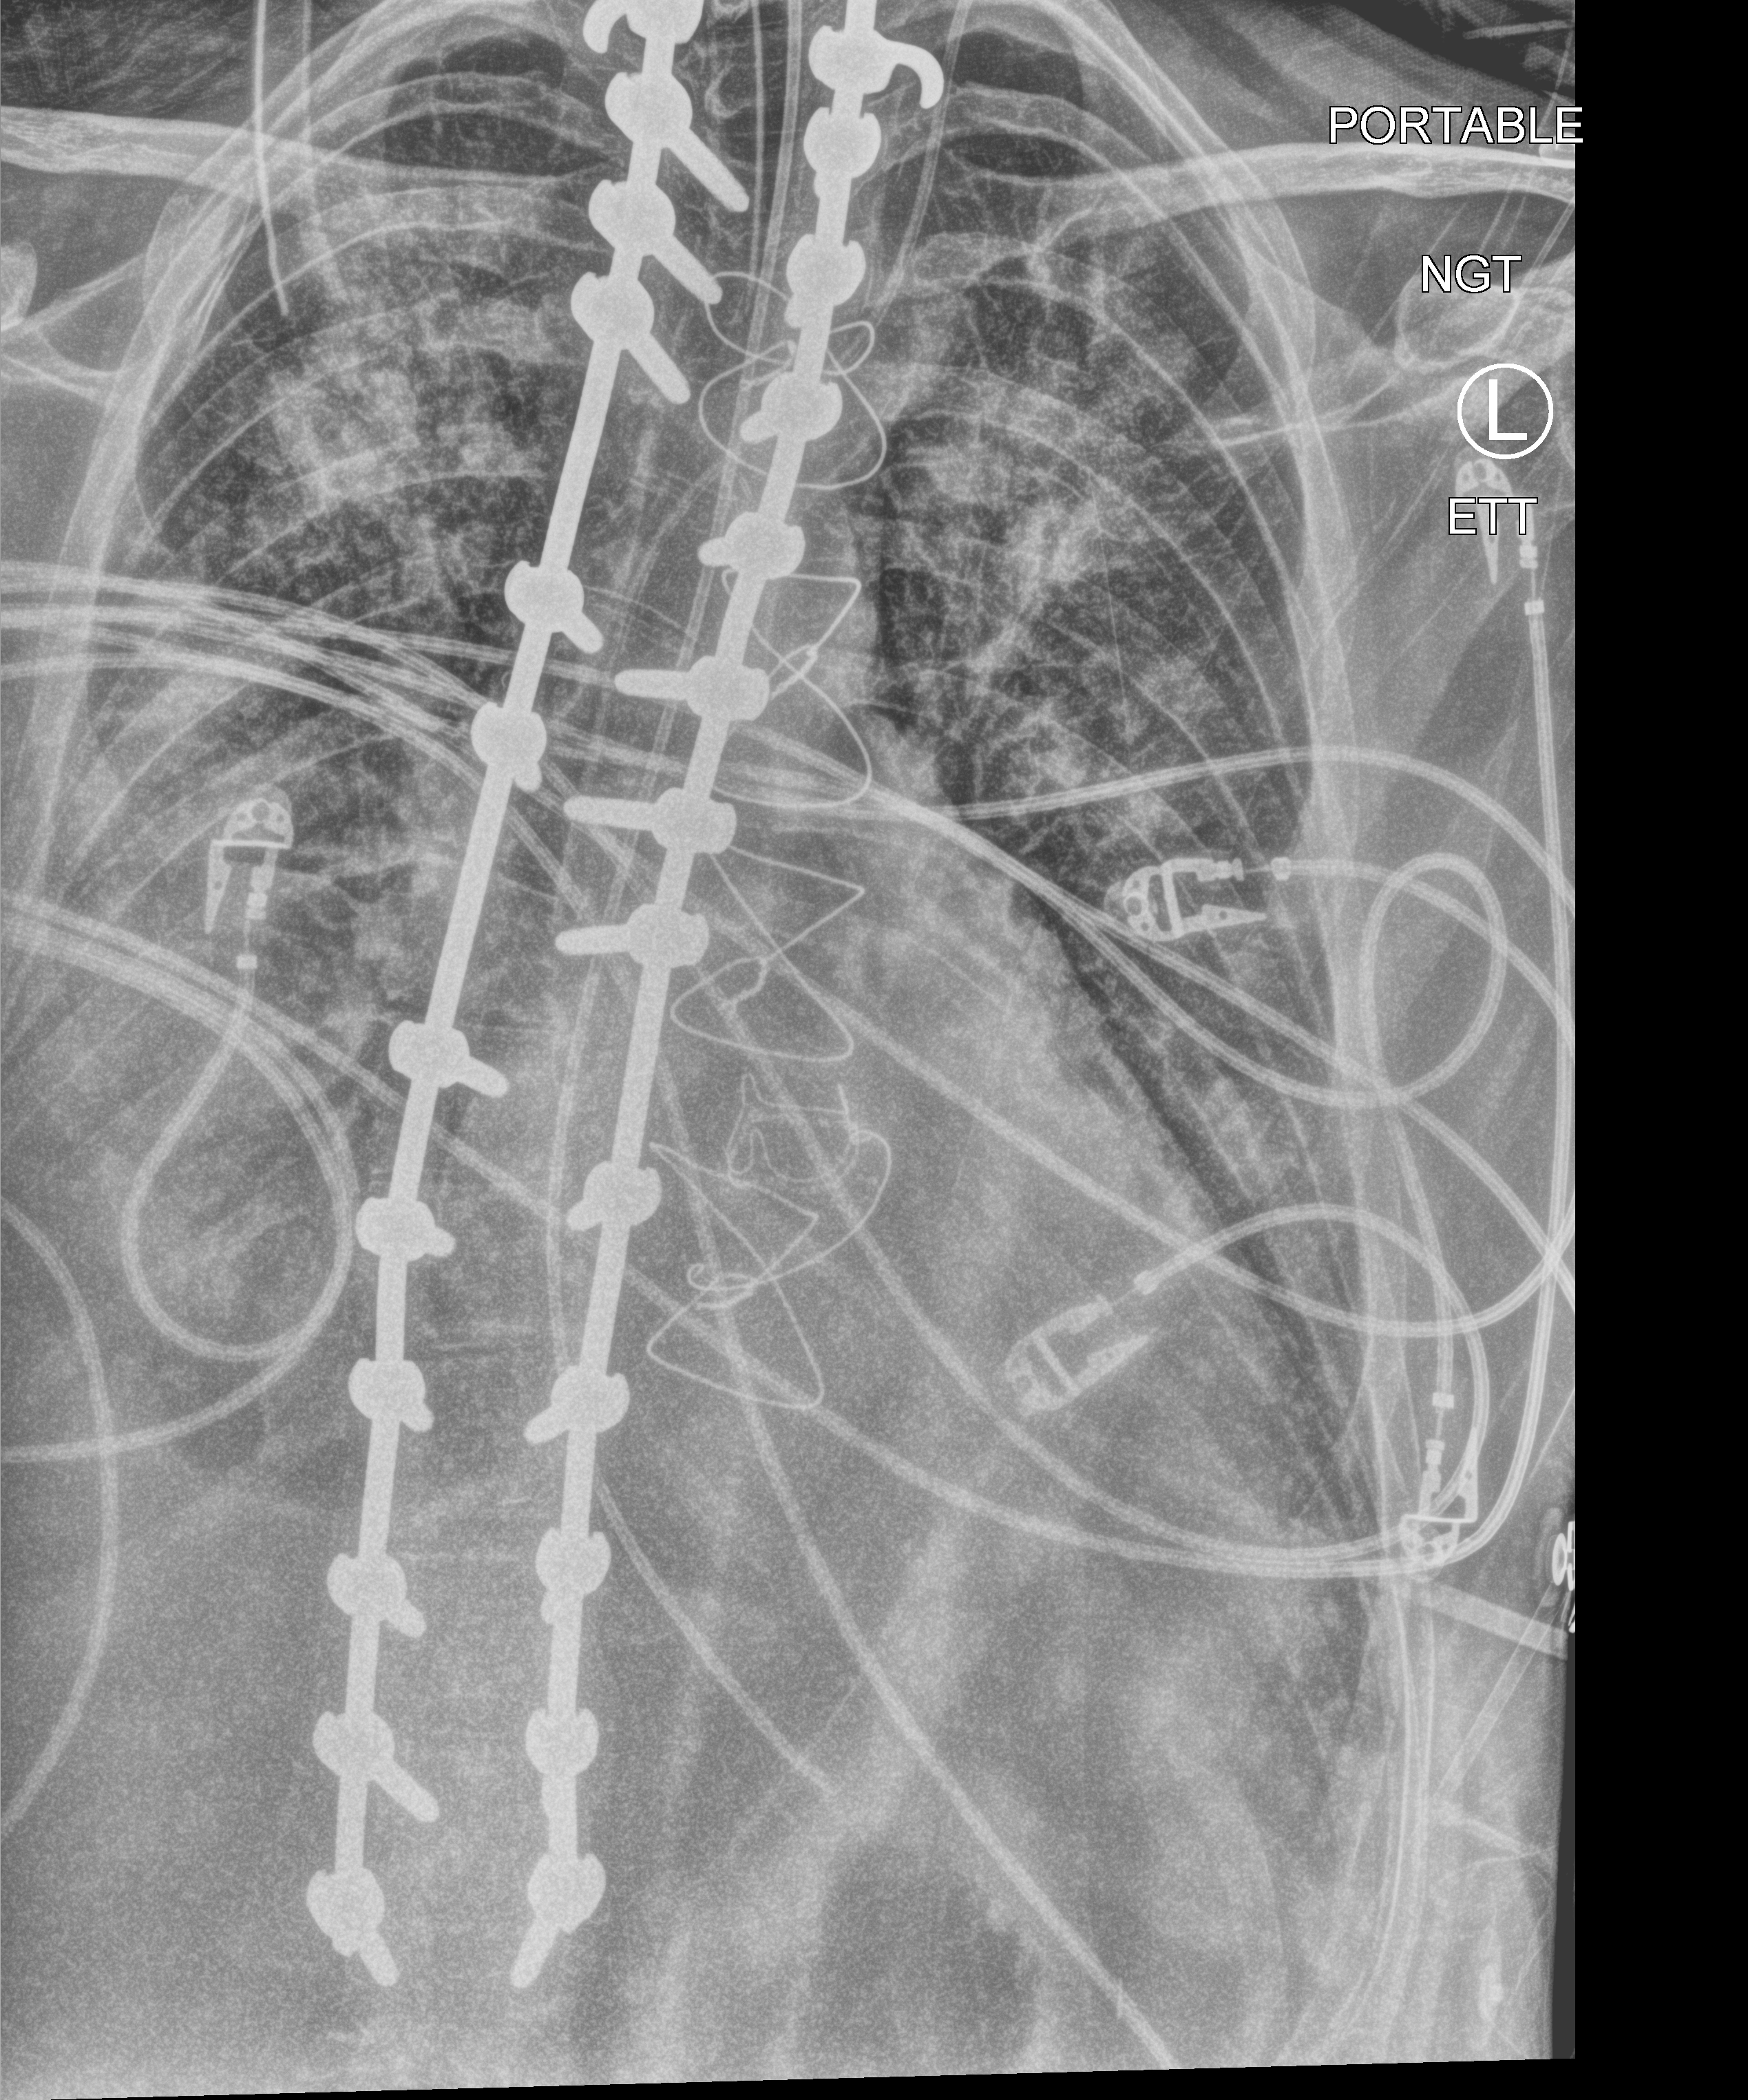
Chest X-ray (portable); anteroposterior (AP) projection. Patient hospitalised with COVID-19, aged 18–59 years.
Admission-level facts for this patient (not findings on this image; timing relative to this image not recorded): COPD (admission record): no; mechanically ventilated during this hospital stay: yes; chronic kidney disease (admission record): no.